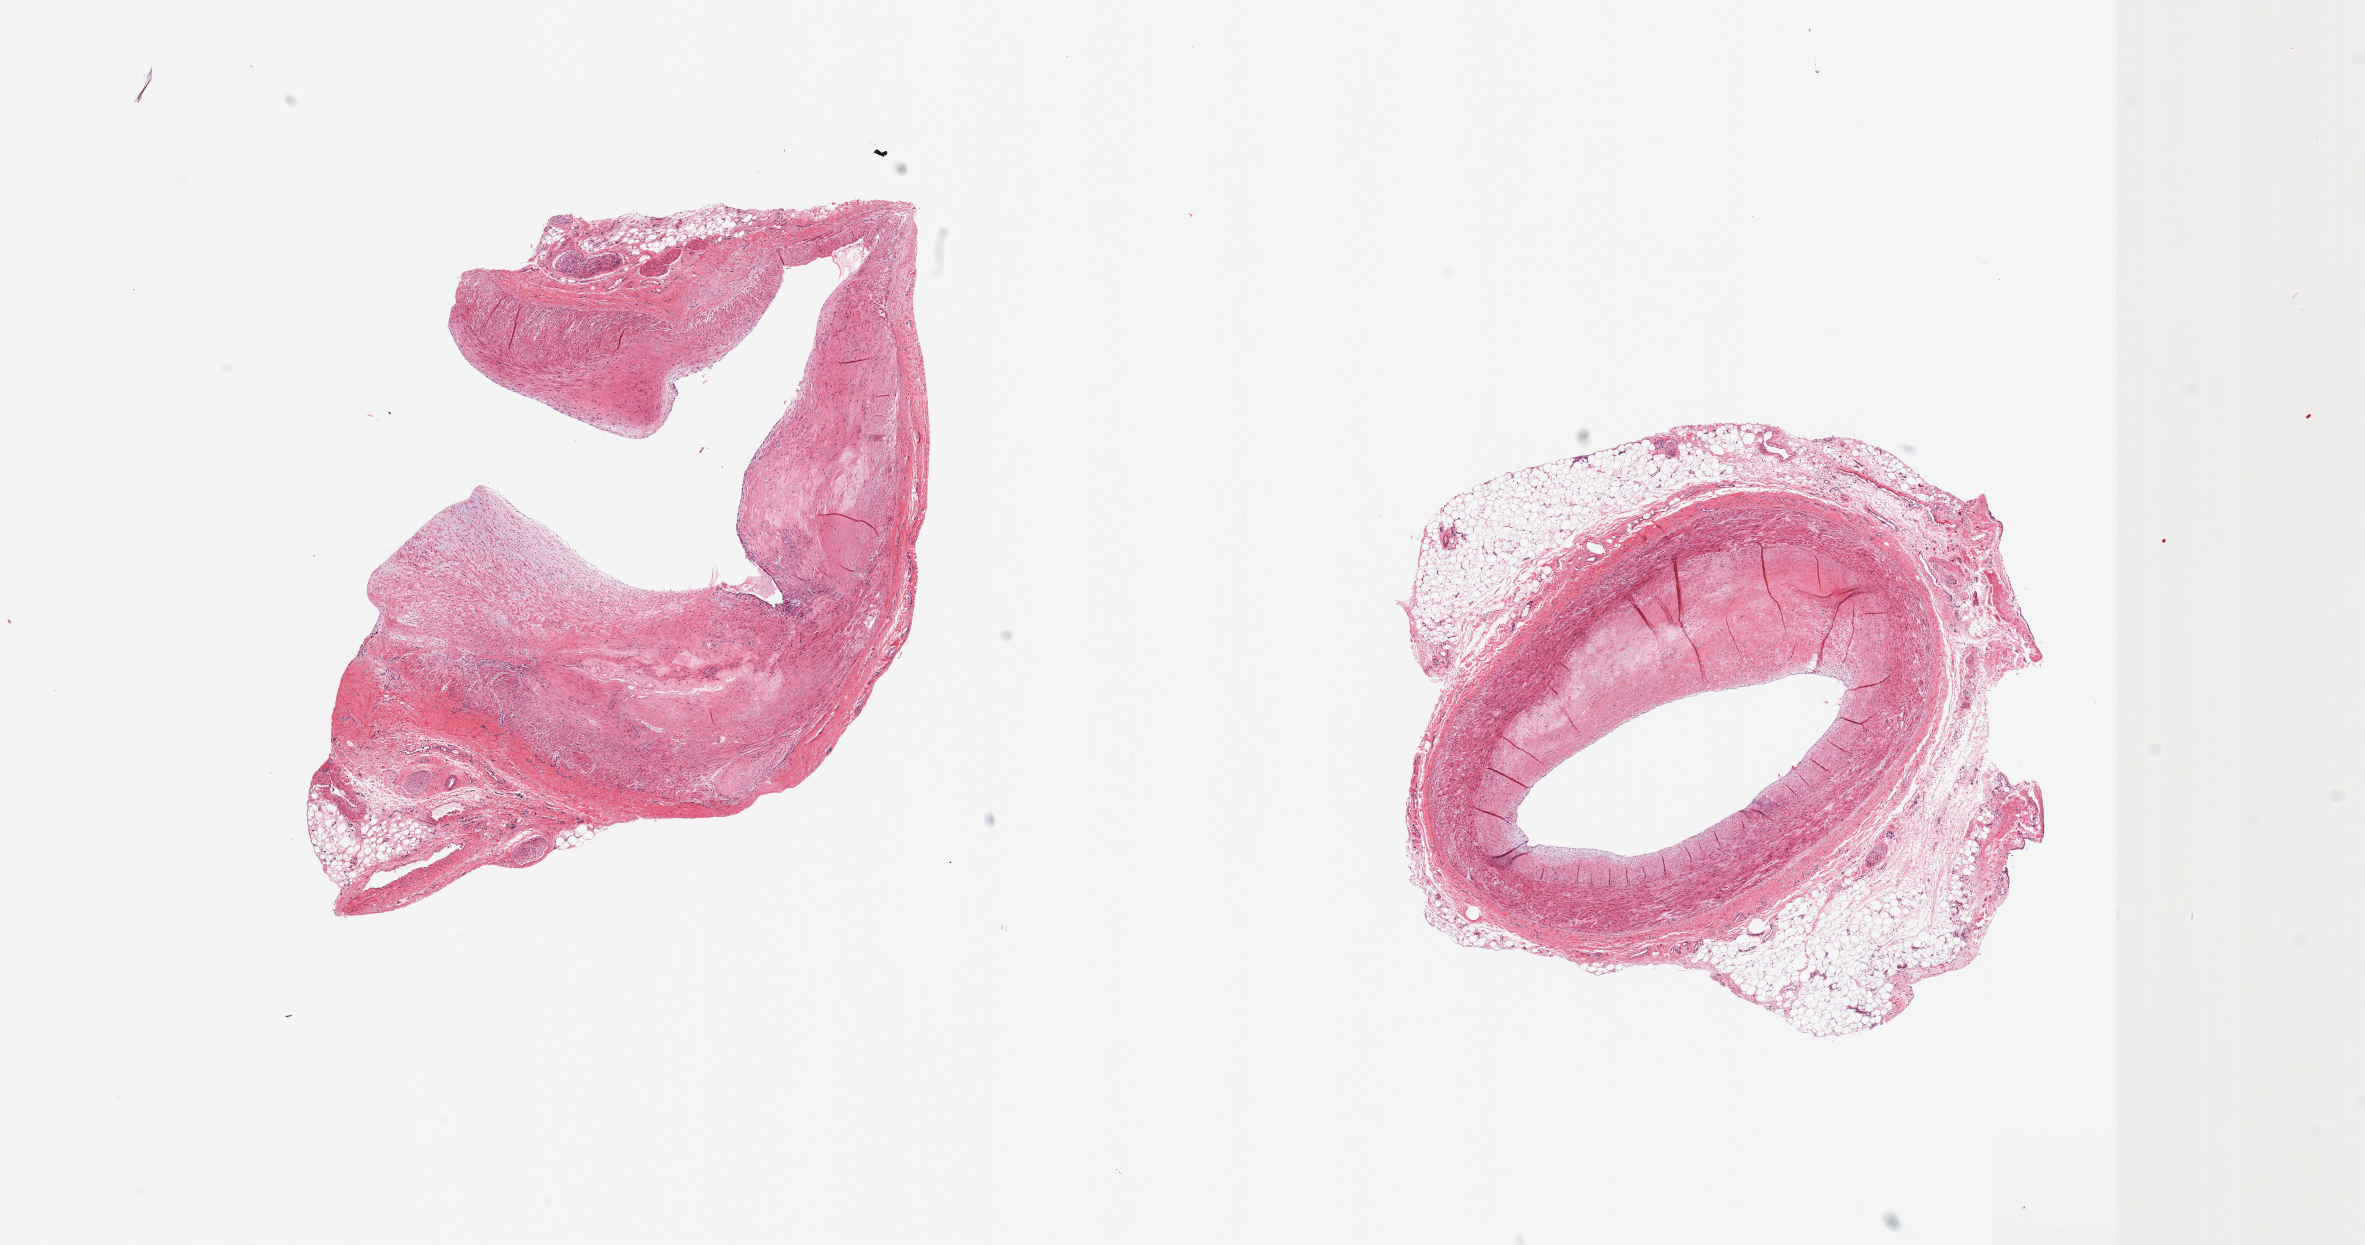
H&E whole-slide image, a low-resolution overview of the entire scanned area, about 18.7 x 9.8 mm (acquisition: 20x scan), PAXgene-fixed paraffin-embedded (PFPE) section, sampled site (target tissue): coronary artery, donor tissue sample. Donor: female.
Reviewer comment on this tissue sample: 2 pieces, 60% occlusive atherosis prominent rims or nubbins of adherent fat up to ~1.5mm, both sections.